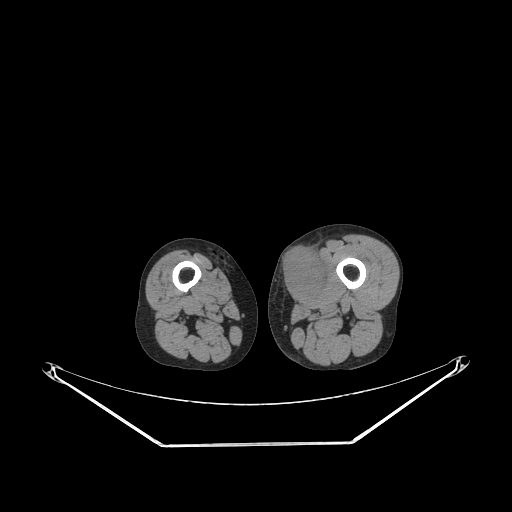
CT of an extremity soft-tissue mass (from a PET/CT study), one axial slice. Slice 215 of 267 in the series (ordered by position). Reconstruction kernel STANDARD. 140 kVp. Soft-tissue window (W 400 / L 40 HU). 512 × 512 image matrix, field of view 500 × 500 mm. Male patient. Case-level facts recorded for this patient, not image findings: histological type: pleiomorphic leiomyosarcoma; grade: high; site of the primary tumour: left thigh.
Structures marked on this image (expert contour drawn on MRI and transferred to this co-registered scan by the dataset authors):
- gross tumour volume including surrounding oedema: bounding box (x1, y1, x2, y2) in pixels: (279, 249, 330, 300)
- gross tumour volume (mass): (279, 249, 325, 300)